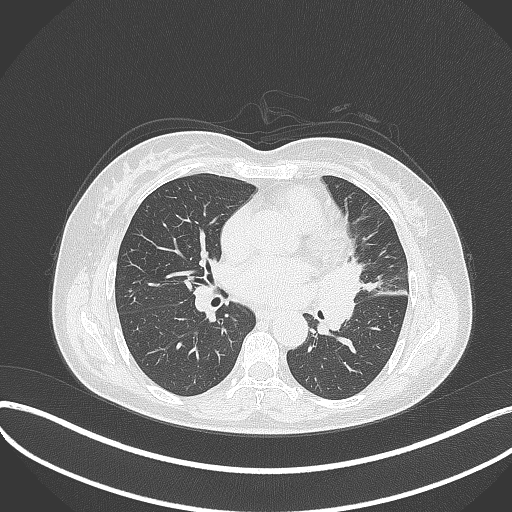
Chest CT, one axial slice. Position 177 of 373 along the scan axis. Reconstruction kernel B70f. 120 kVp. Lung window (W 1500 / L -600 HU). 1 mm slice thickness. 512 × 512 image matrix, field of view 400 × 400 mm. Patient: female, 54 years. Case-level facts recorded for this patient, not image findings: clinical TNM (as recorded): T2a N1 M0; histopathological grade: G3.
Outlined on this slice (bounding box drawn by a radiologist):
- lung tumour (recorded histology: small cell carcinoma): box from (x=322, y=259) to (x=373, y=333) px